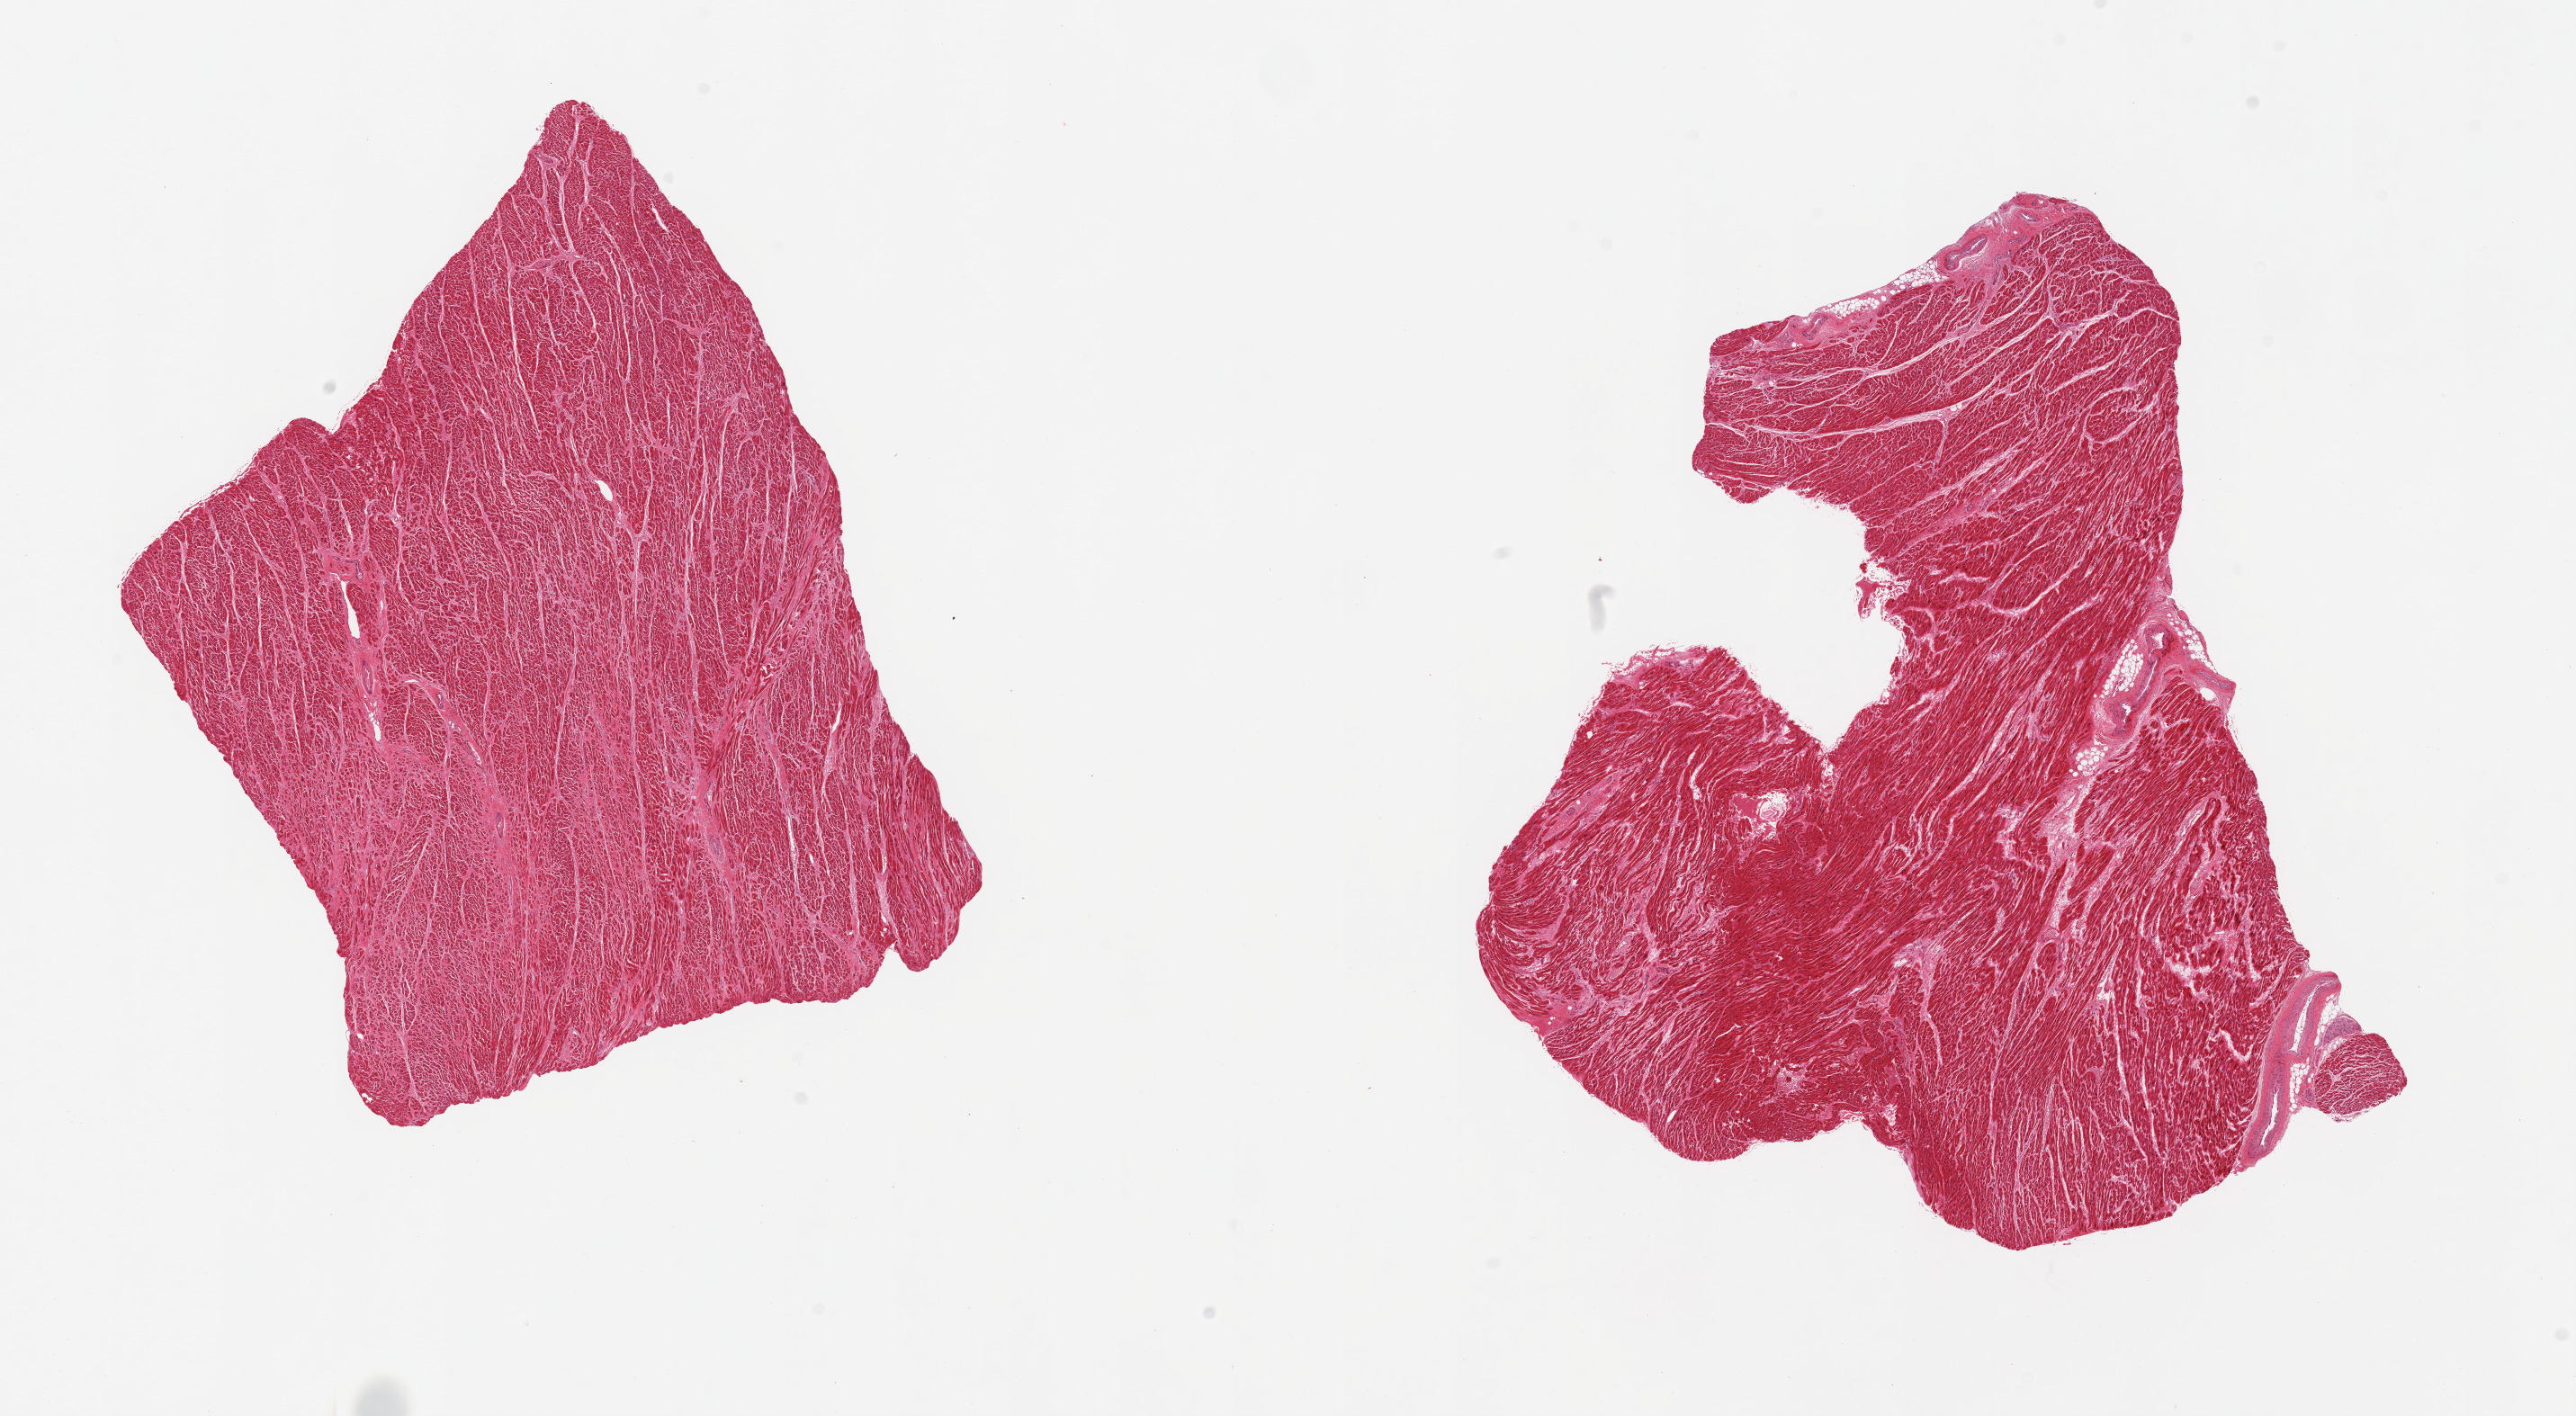
Whole-slide image, haematoxylin and eosin stain, brightfield — whole scanned area (about 22.6 x 12.4 mm) shown as a low-resolution overview, PAXgene-fixed paraffin-embedded (PFPE) section, target tissue: heart, donor tissue sample. Donor sex: female.
Review note (as recorded): 2 pieces; patchy and diffuse interstitial fibrosis, hypertrophy.